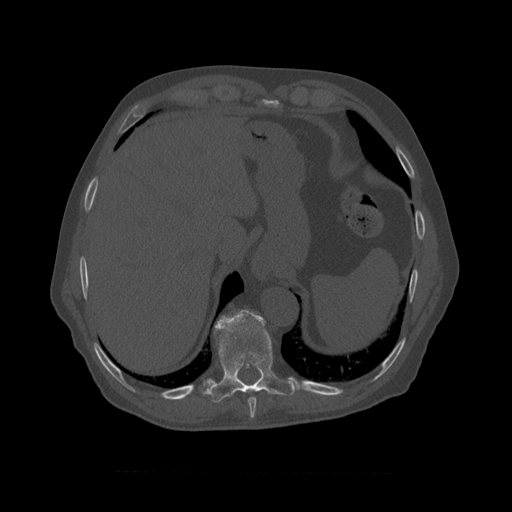
CT including the spine, one axial slice; slice 426 of 450 in the series (ordered by position); reconstruction kernel STANDARD; 120 kVp; bone window (W 1800 / L 400 HU); 1.25 mm slice thickness; 512 × 512 image matrix, field of view 405 × 405 mm. Patient age 75 years. Case-level facts recorded for this patient, not image findings: primary cancer: prostate.
Outlined on this slice (semi-automatic segmentation, software-assisted and operator-edited):
- T8 vertebra: bounding box [x1, y1, x2, y2] px = [248, 397, 257, 410]
- T9 vertebra: [213, 310, 295, 398]